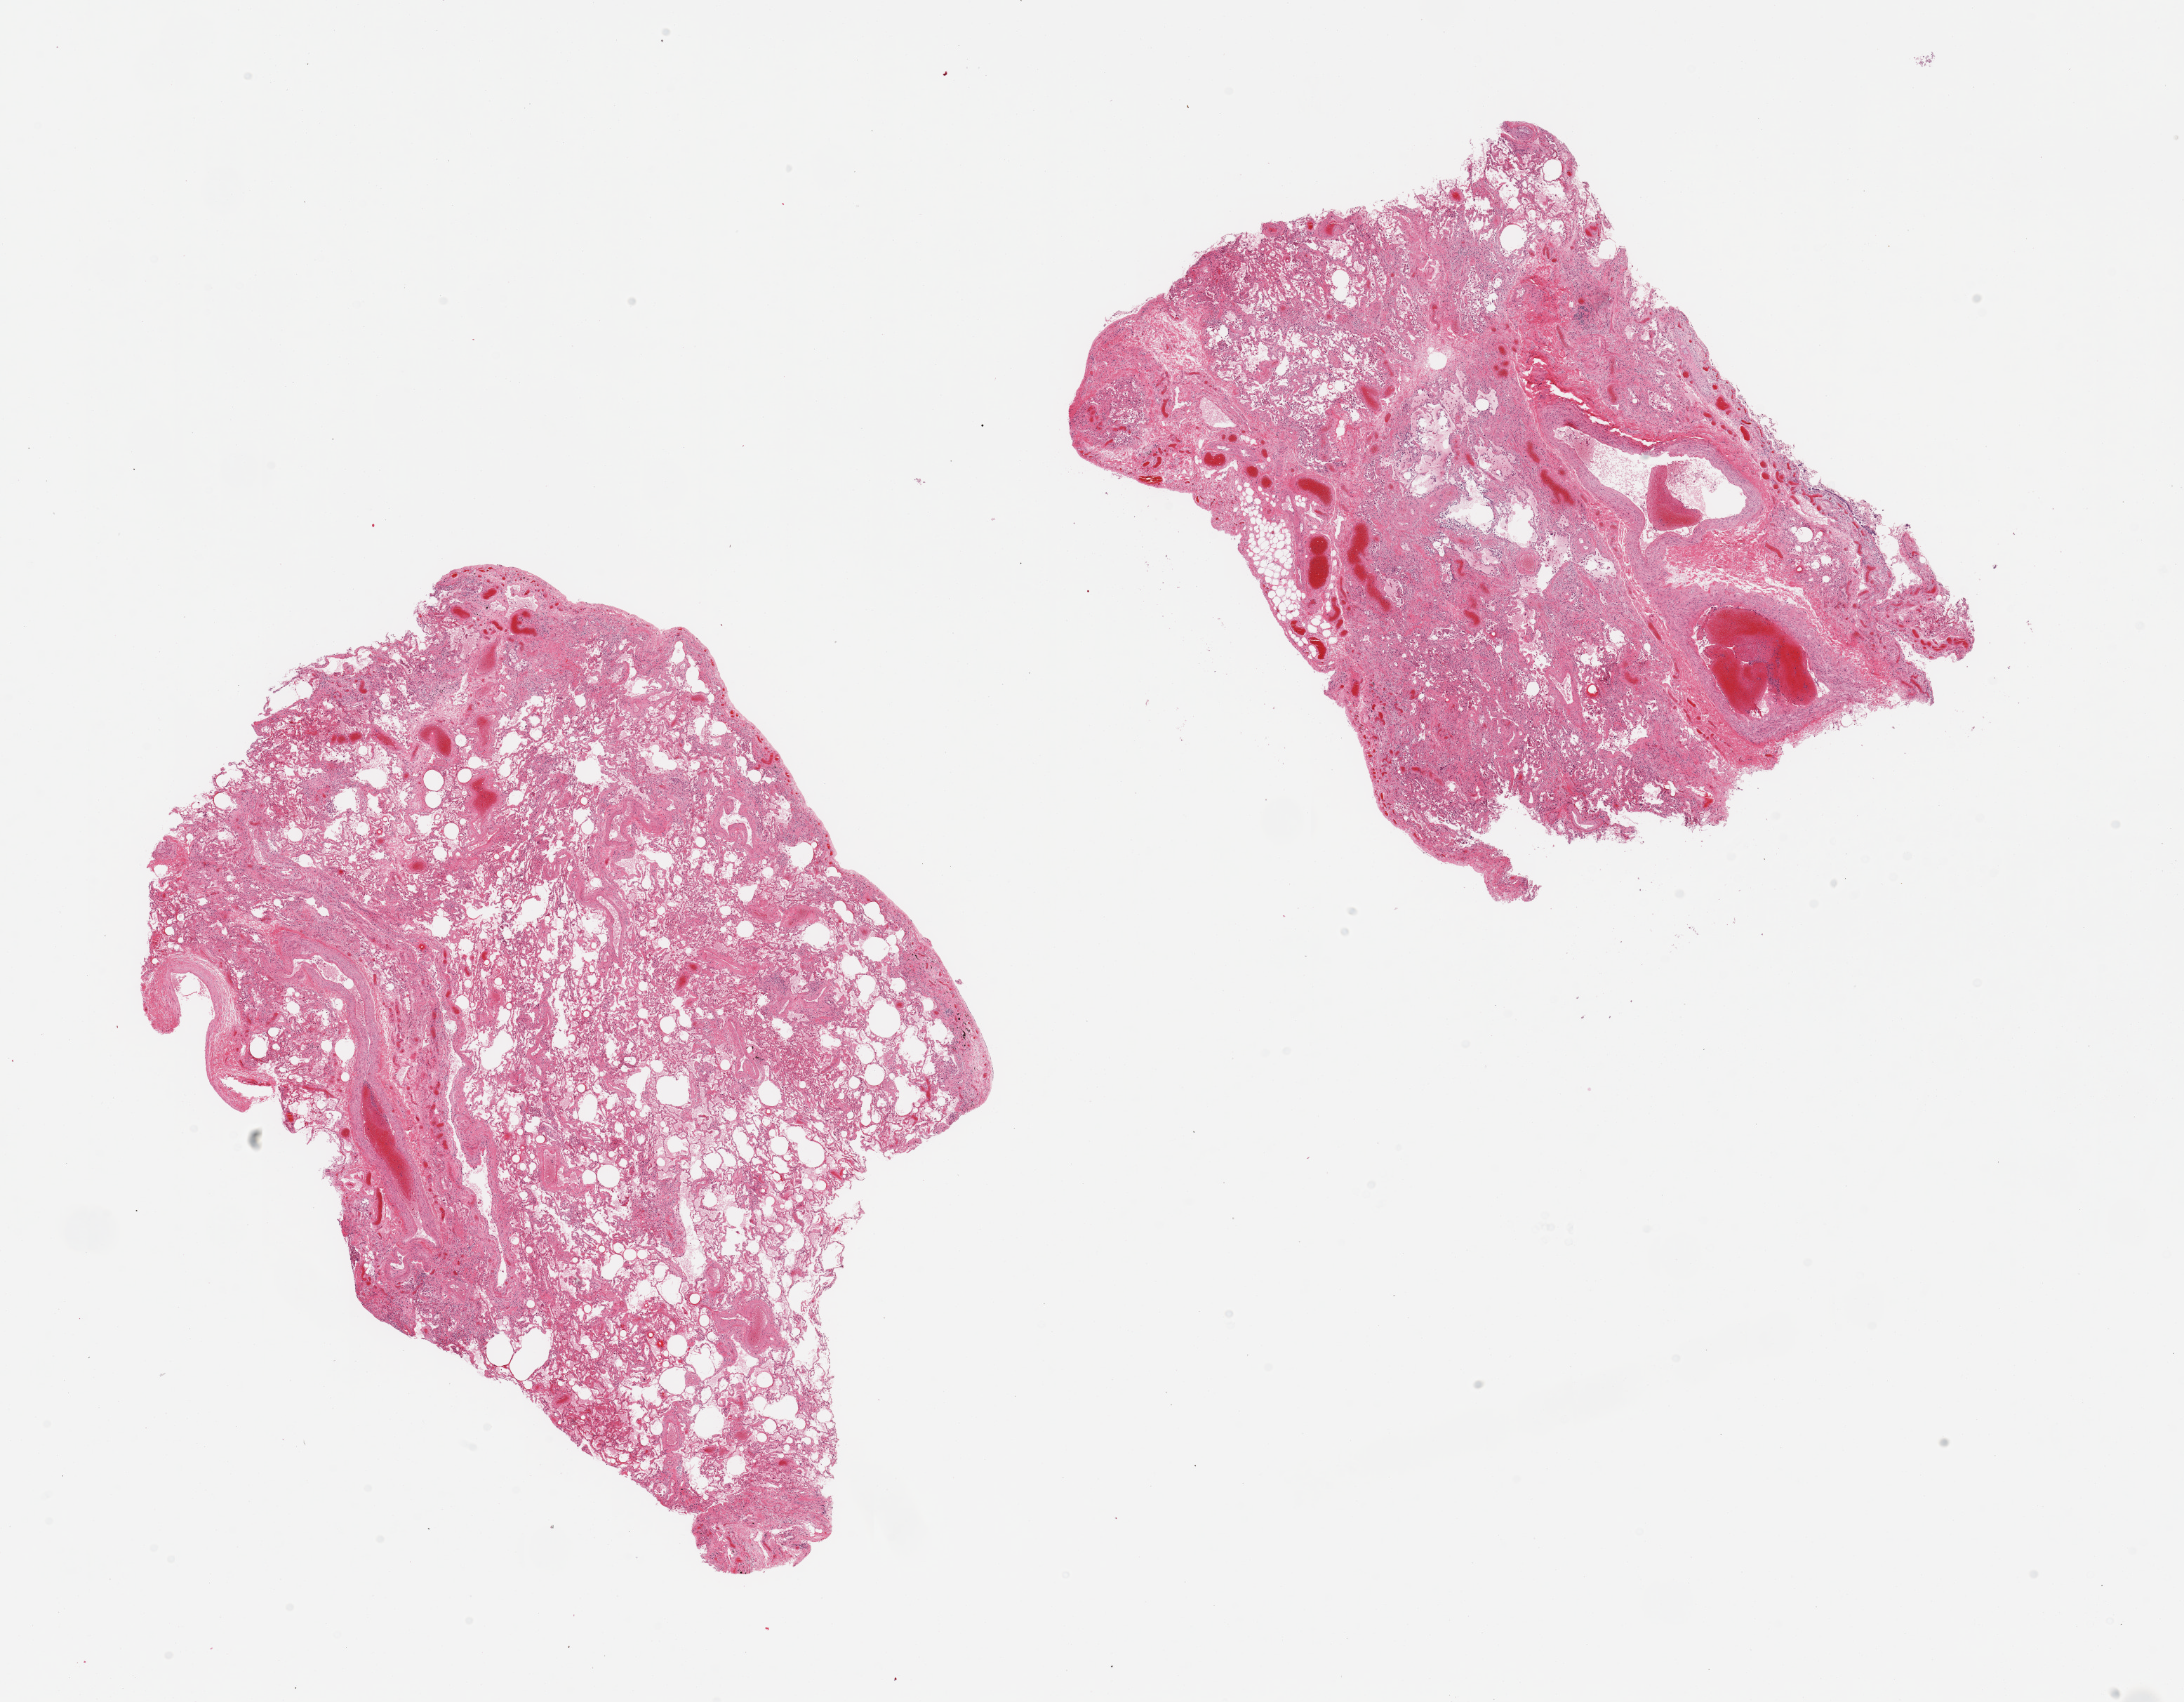
Haematoxylin and eosin whole-slide image, brightfield, a low-resolution overview of the entire scanned area, about 24.6 x 19.2 mm (slide scanned at 20x); PAXgene-fixed, paraffin-embedded tissue; section of lung (target tissue); tissue donor sample. Donor sex: male.
Pathologist's review note for this sample: 2 pieces; areas of moderate fibrosis, alveolar edema and macrophages; large vein occupies 20% of 1 piece.